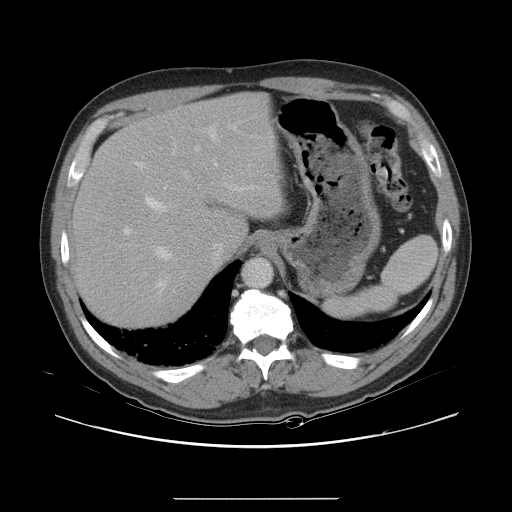
Contrast-enhanced abdominal CT, one axial slice; slice 22 of 40 in the series (ordered by position); intravenous contrast given; soft-tissue window (W 400 / L 40 HU); 5 mm slice thickness; 512 × 512 image matrix, field of view 408 × 408 mm. Male patient, age 64 years. From the clinical record (not read from this slice): diagnosis: colorectal cancer liver metastases, imaged before liver resection; multiple liver metastases: yes; largest metastasis: 3.2 cm.
Outlined on this slice (outlined manually by an expert reader):
- hepatic veins: box from (x=136, y=131) to (x=217, y=294) px
- liver: (x=75, y=94)–(x=281, y=327)
- planned liver remnant (the part of the liver to remain after resection): (x=76, y=95)–(x=280, y=263)
- portal vein (with intrahepatic branches): (x=124, y=147)–(x=259, y=235)